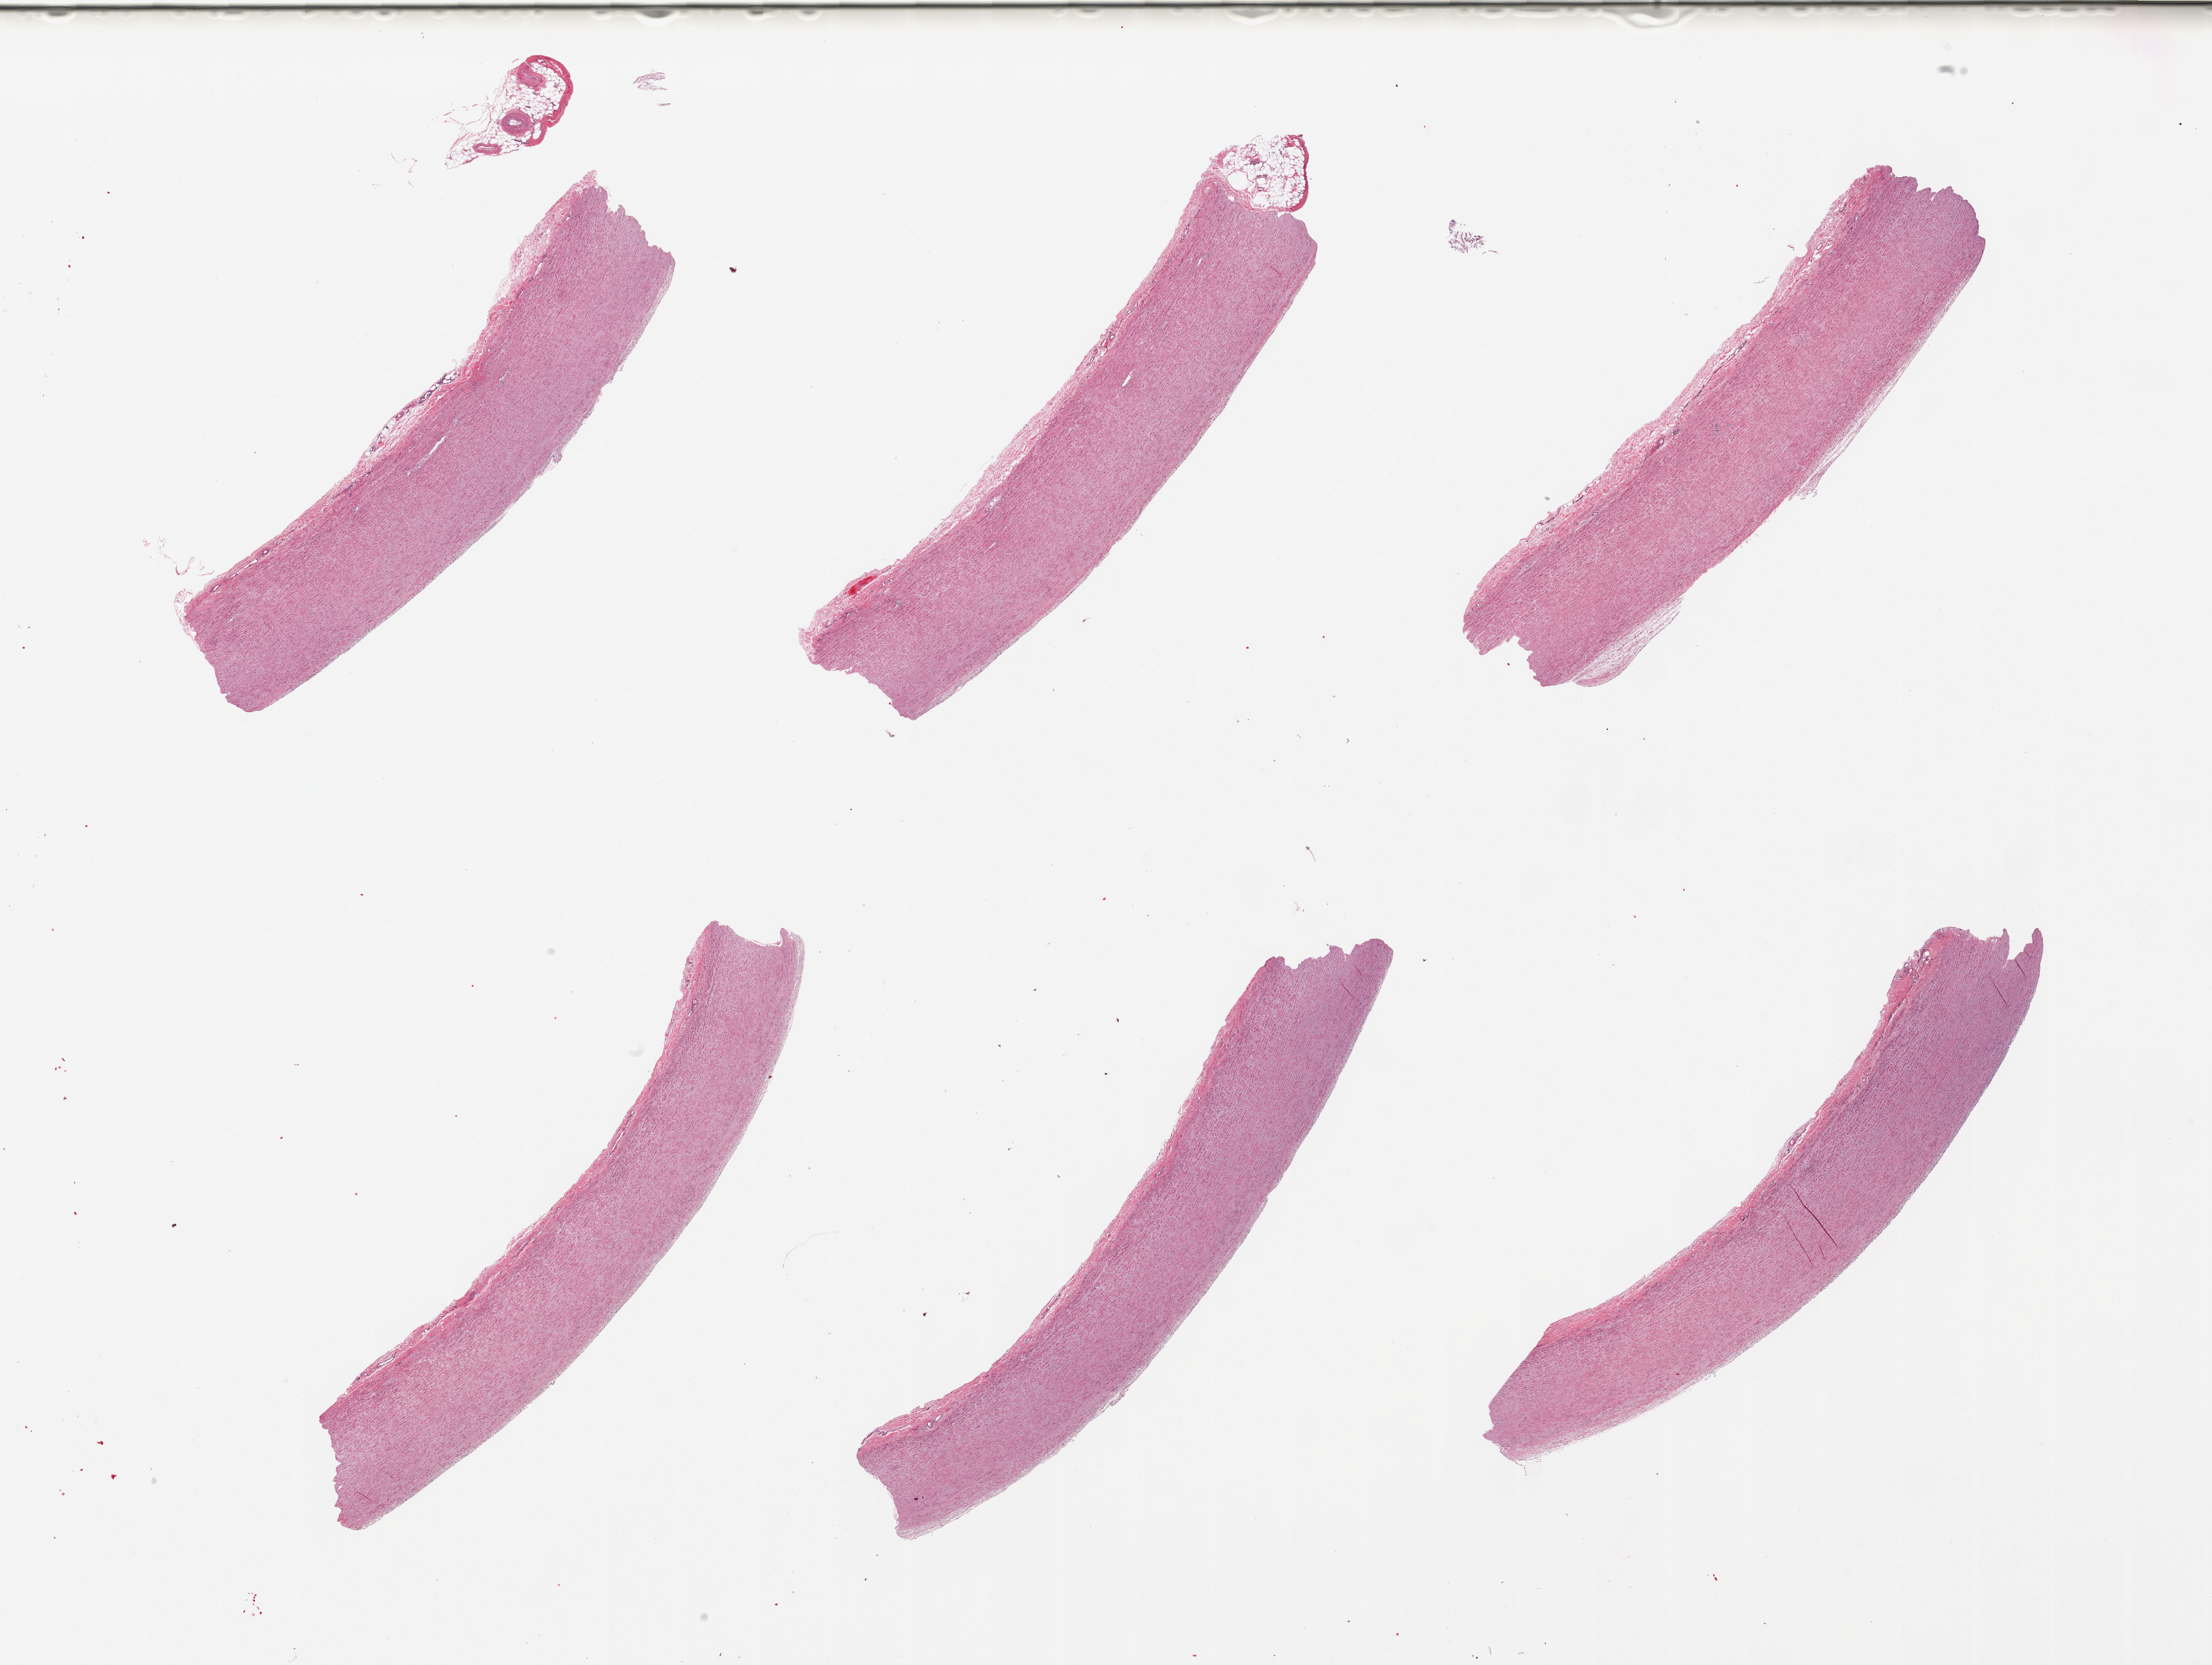
Whole-slide image, hematoxylin and eosin (H&E) stain, a low-resolution overview of the entire scanned area, about 28.5 x 21.5 mm; PAXgene-fixed, paraffin-embedded tissue; sampled site (target tissue): aorta; donor tissue sample. Female donor.
Review note (as recorded): 6 pieces, minimal atherosis.